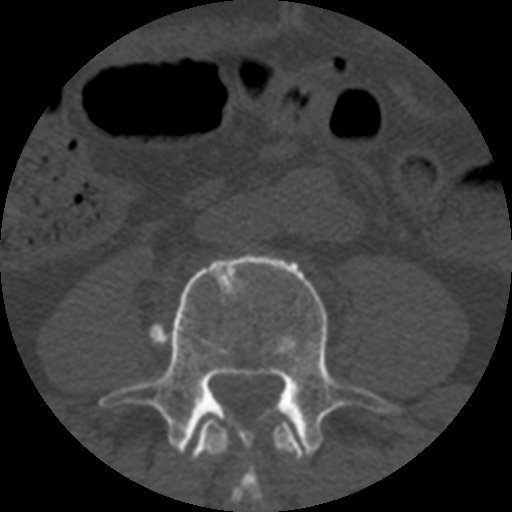
CT including the spine, one axial slice; slice 97 of 508 in the series (ordered by position); reconstruction kernel STANDARD; 120 kVp; bone window (W 1800 / L 400 HU); 512 × 512 image matrix. Patient age 57 years. From the clinical record (not read from this slice): primary cancer: prostate.
Structures marked on this image (semi-automatic segmentation, software-assisted and operator-edited):
- L3 vertebra: bounding box (x1, y1, x2, y2) in pixels: (190, 415, 304, 504)
- L4 vertebra: (99, 253, 401, 493)